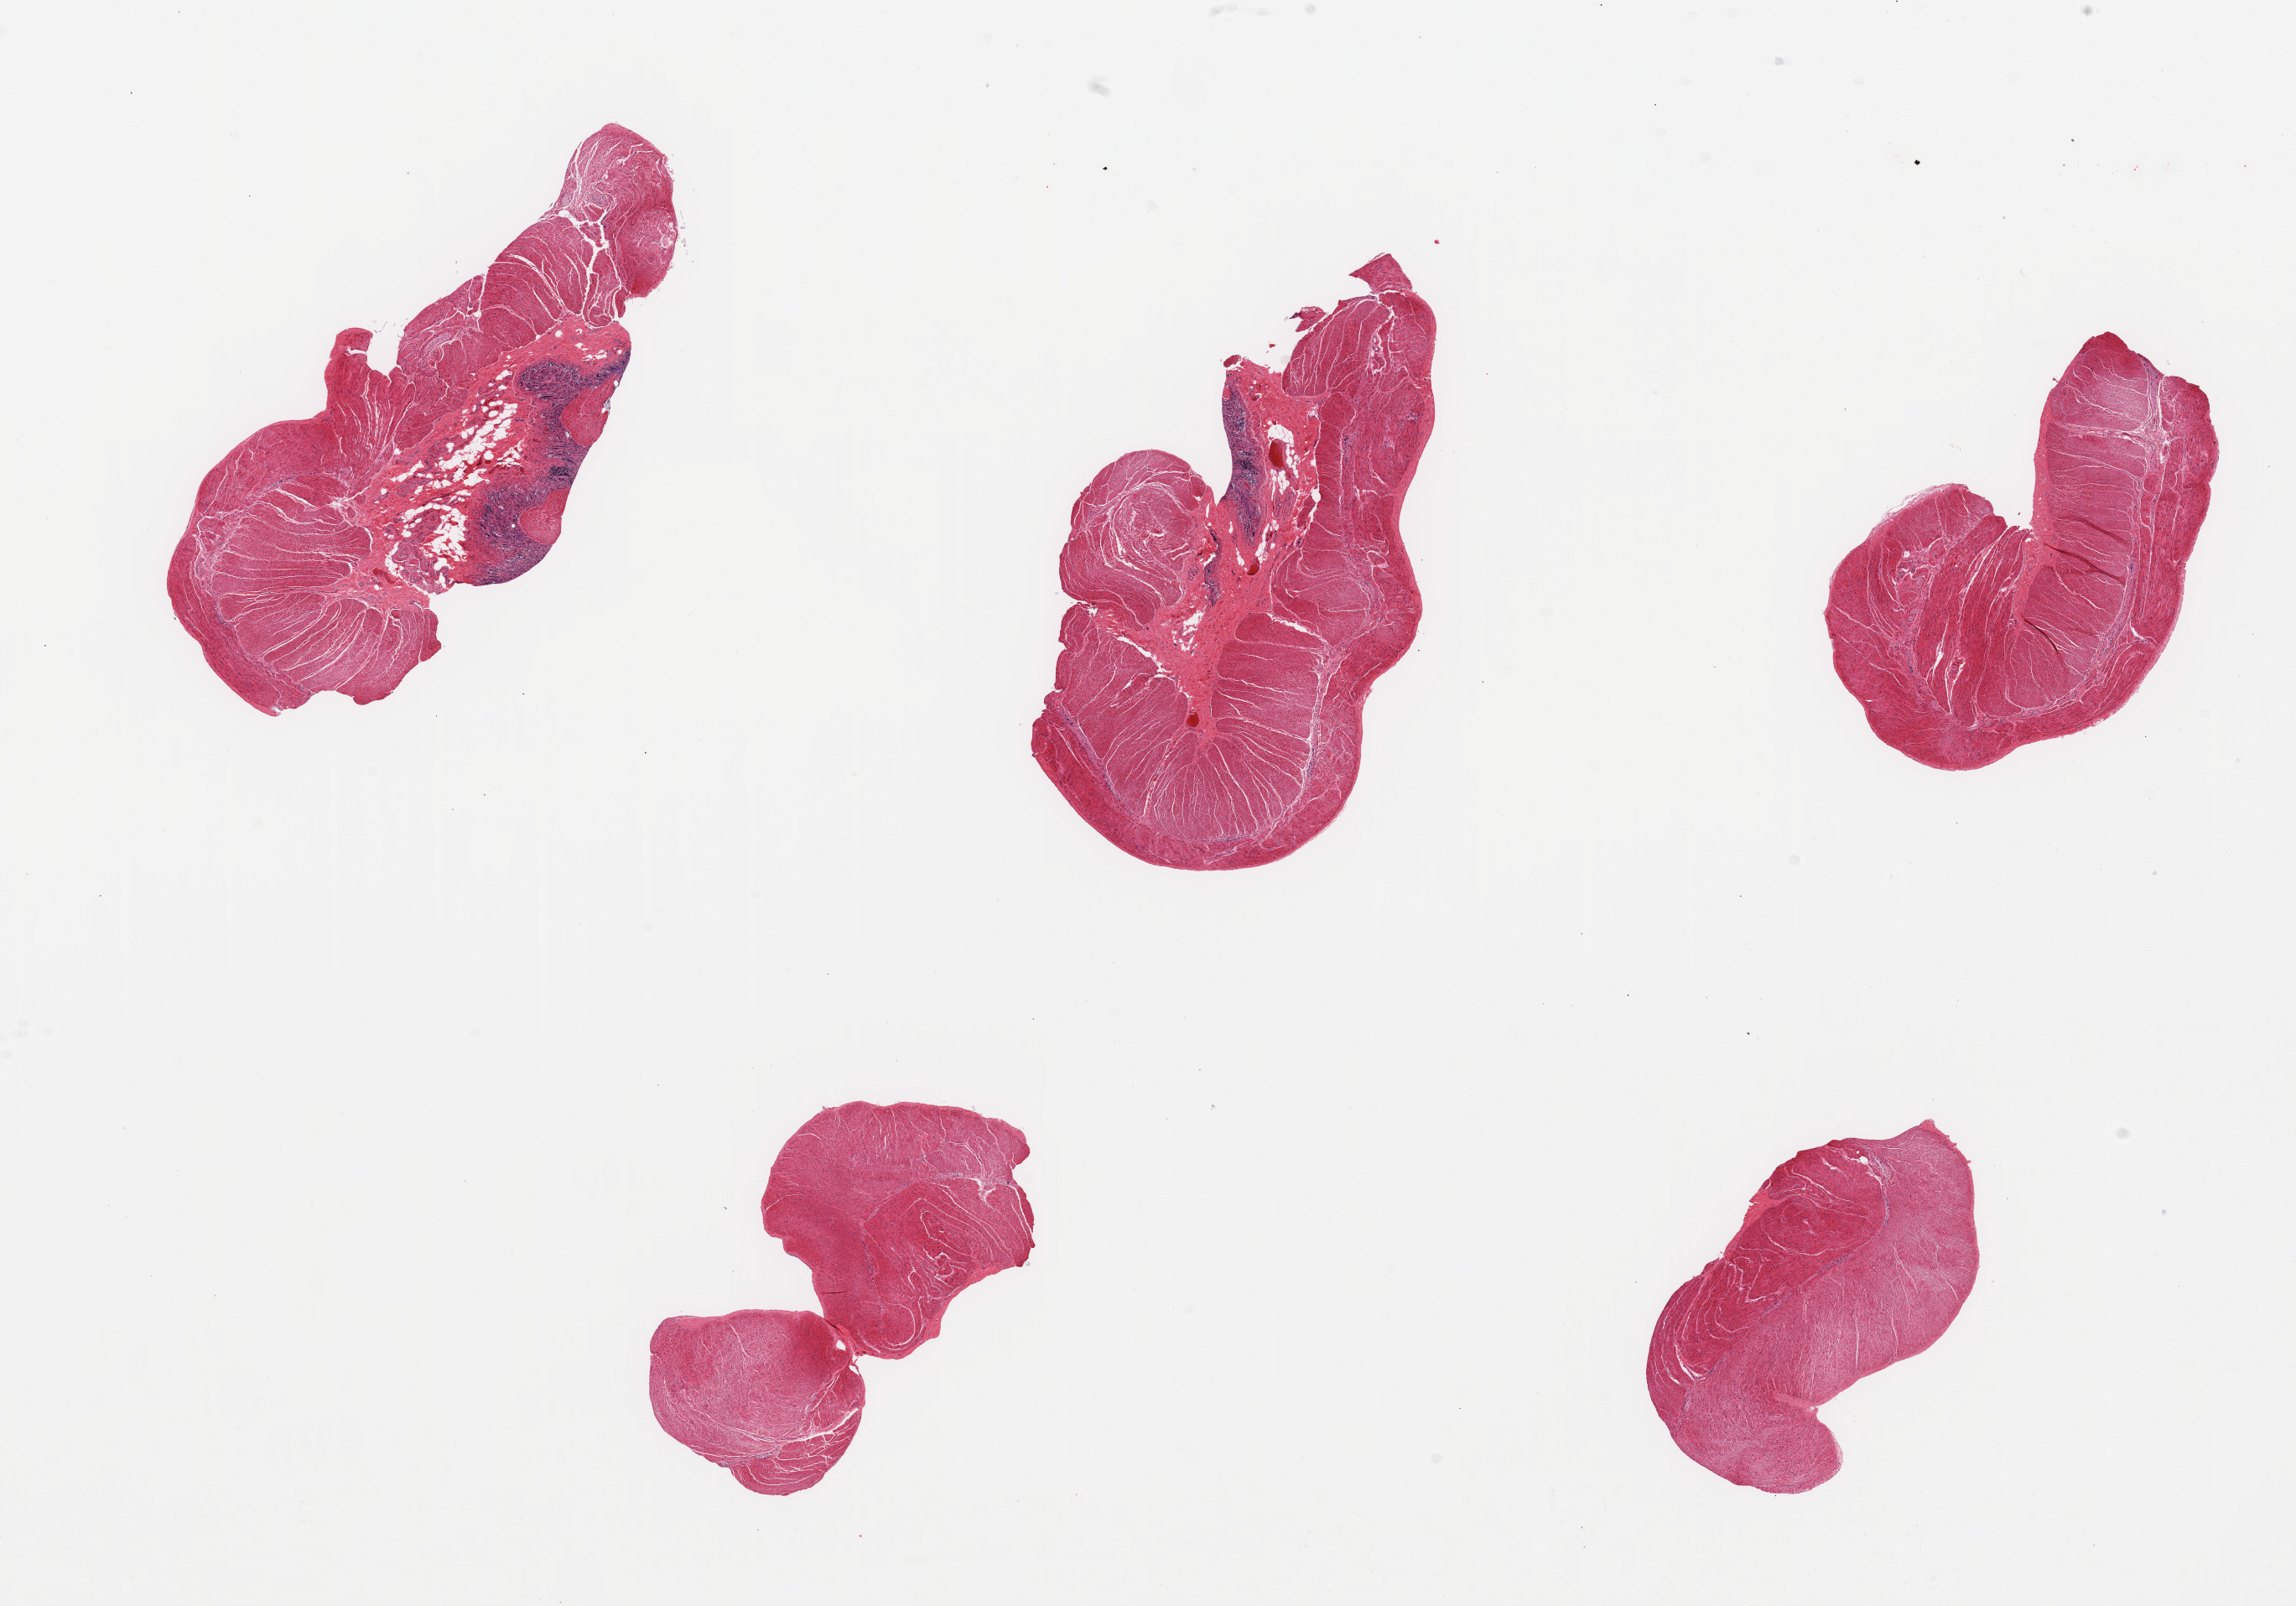
H&E whole-slide image — a low-resolution overview of the entire scanned area, about 21.7 x 15.1 mm (acquisition: 20x scan), PAXgene-fixed, paraffin-embedded tissue, target tissue: sigmoid colon, tissue donor sample.
Review note (as recorded): 5 pieces: 2 with 20 & 30% autolyzed mucosa & submucosa; ample muscle.